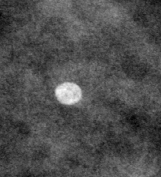
Crop from a digitized film mammogram around one marked abnormality; left breast; CC view.
Finding: calcifications, morphology lucent center; BI-RADS assessment category 2; subtlety rating 4 on a 1 (subtle) to 5 (obvious) scale; benign; no additional work-up was recommended (benign without callback).